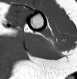
MRI of an extremity soft-tissue mass, one axial slice. Position 4 of 28 along the scan axis. MR volume resampled by the dataset authors to the PET/CT grid (not the native acquisition matrix). 3.27 mm slice thickness. 77 × 79 image matrix, field of view 75 × 77 mm. Female patient. From the clinical record (not read from this slice): histological type: malignant fibrous histiocytoma; grade: low; site of the primary tumour: left arm.
Structures marked on this image (expert contour drawn on MRI and transferred to this co-registered scan by the dataset authors):
- gross tumour volume (mass): bounding box (x1, y1, x2, y2) in pixels: (47, 40, 54, 49)